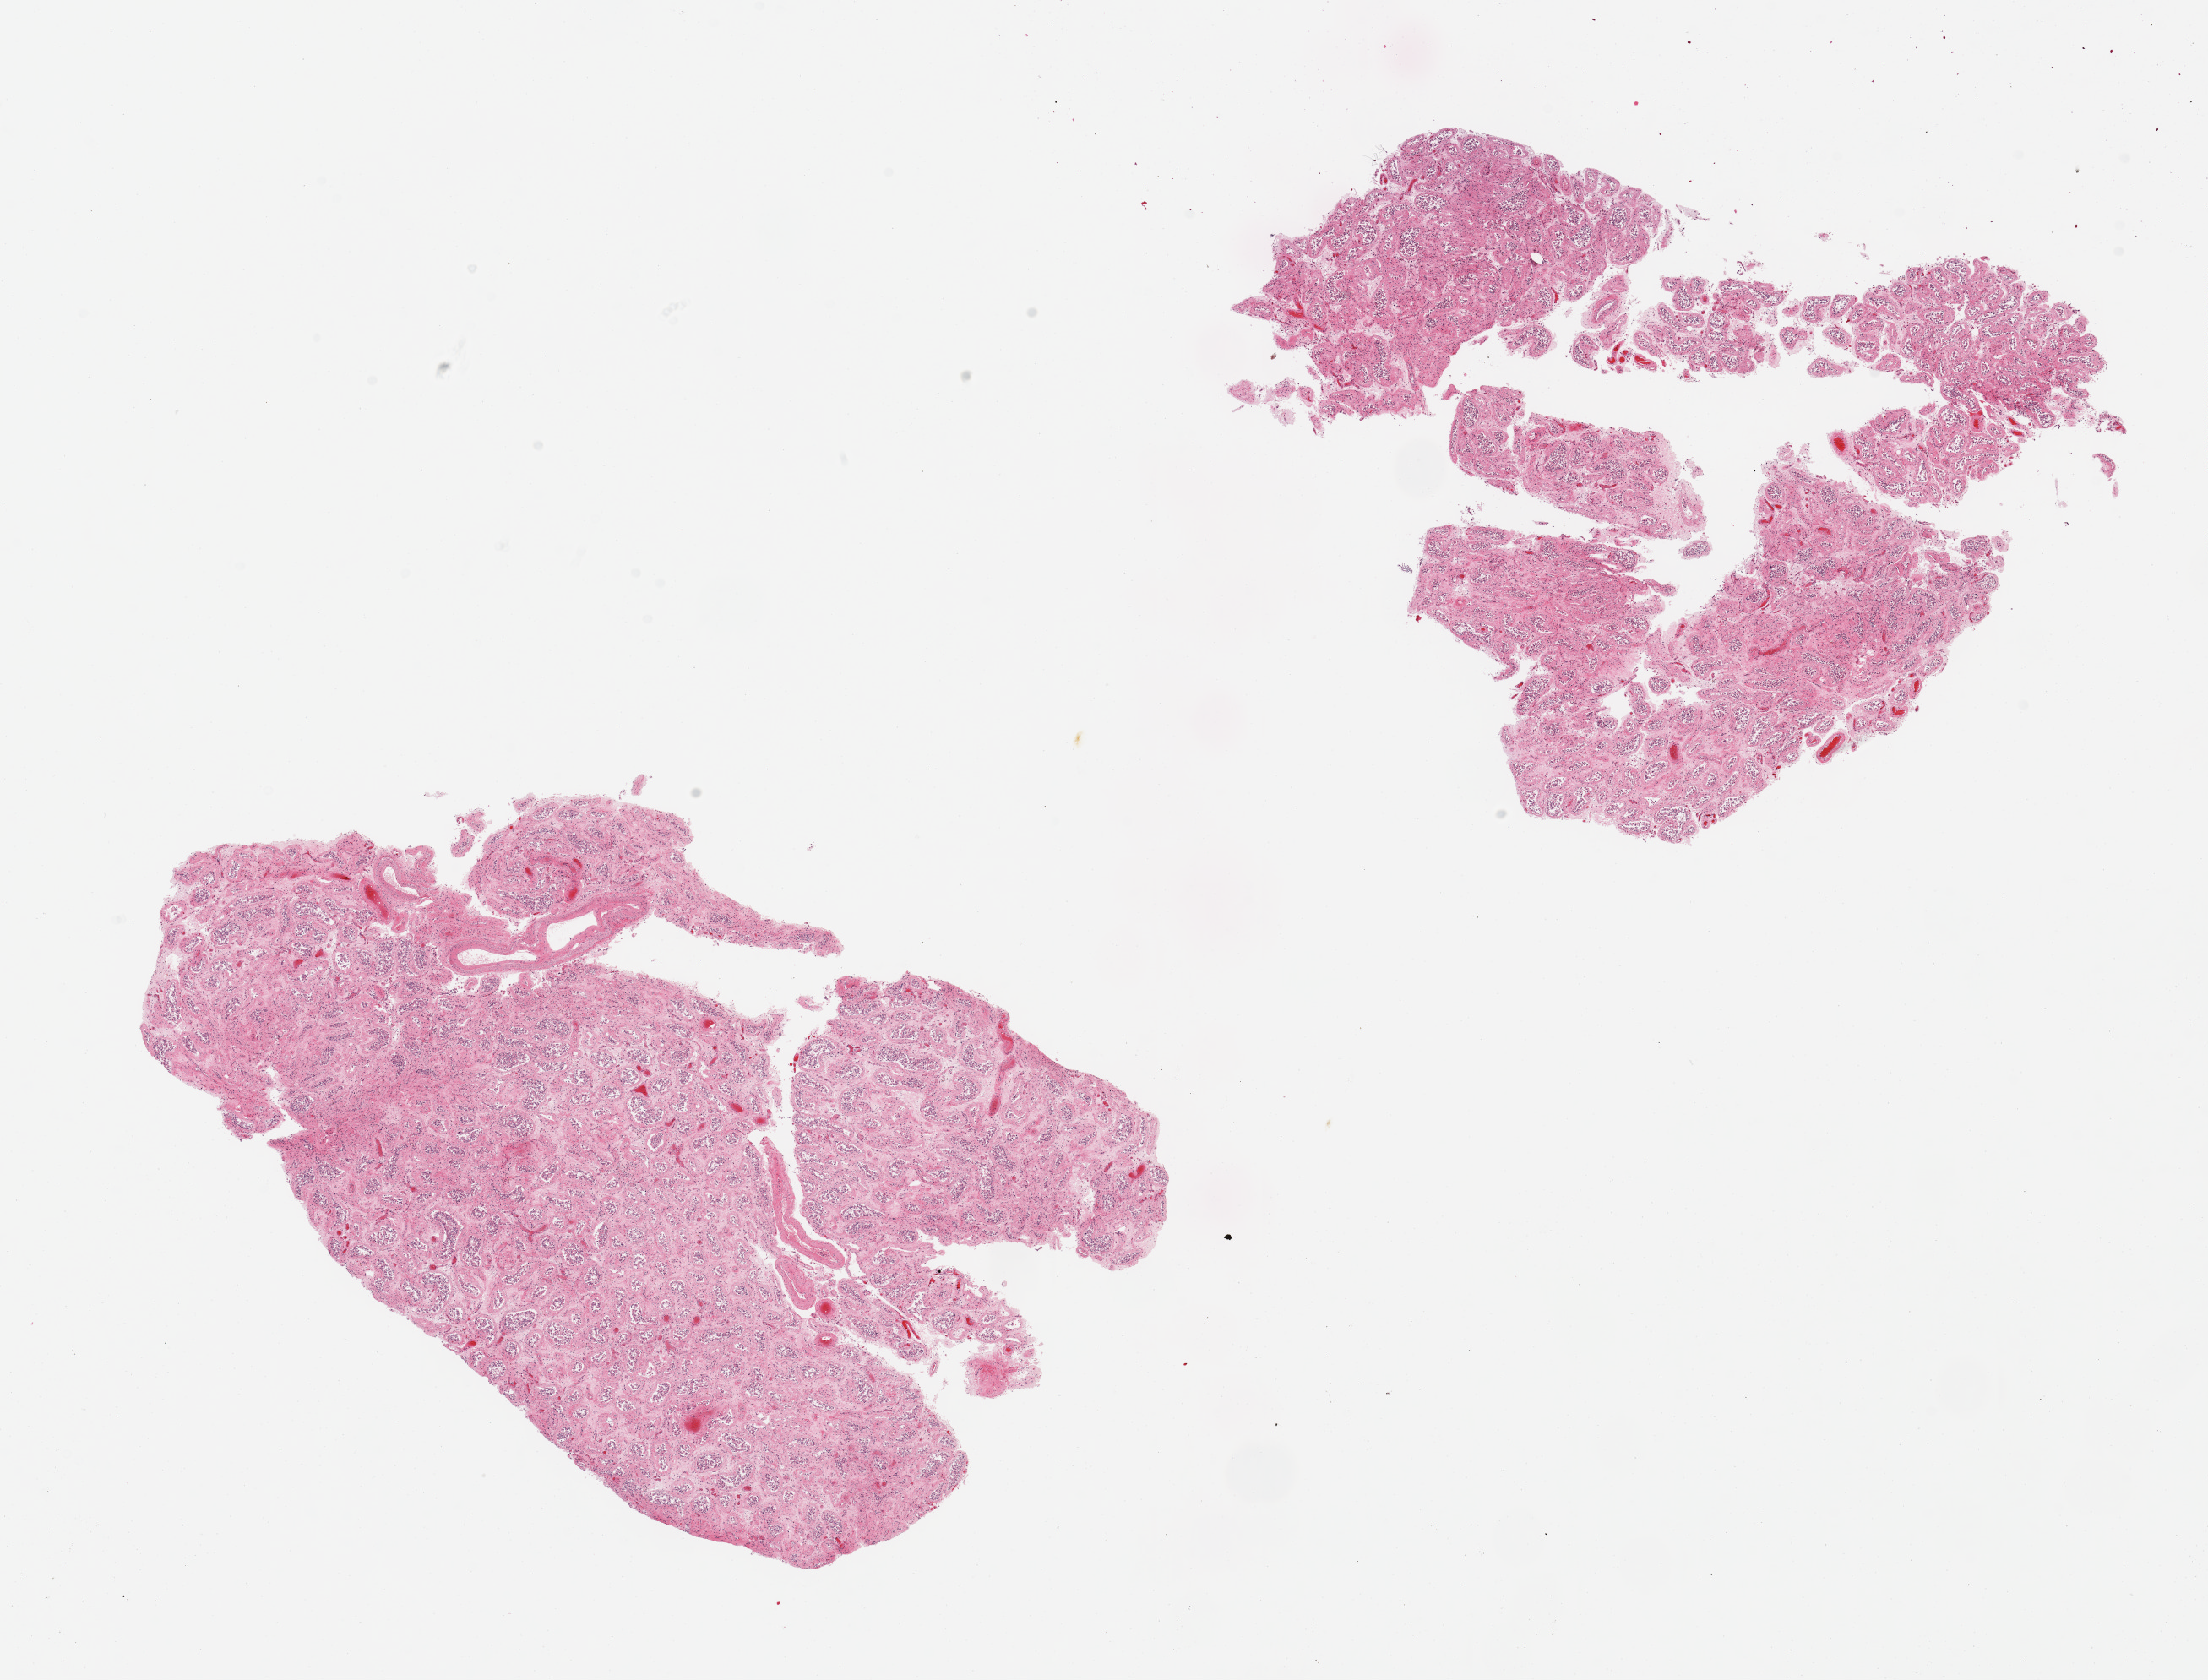
Digitized H&E-stained section, low-resolution overview of the scanned area, about 20.7 x 15.7 mm; PAXgene-fixed, paraffin-embedded tissue; target tissue: testis; tissue donor sample. Donor sex: male.
Reviewer comment on this tissue sample: 2 fragmented pieces; severe fibrosis, hyalinization, autolysis and no obvious spermatogenesis.